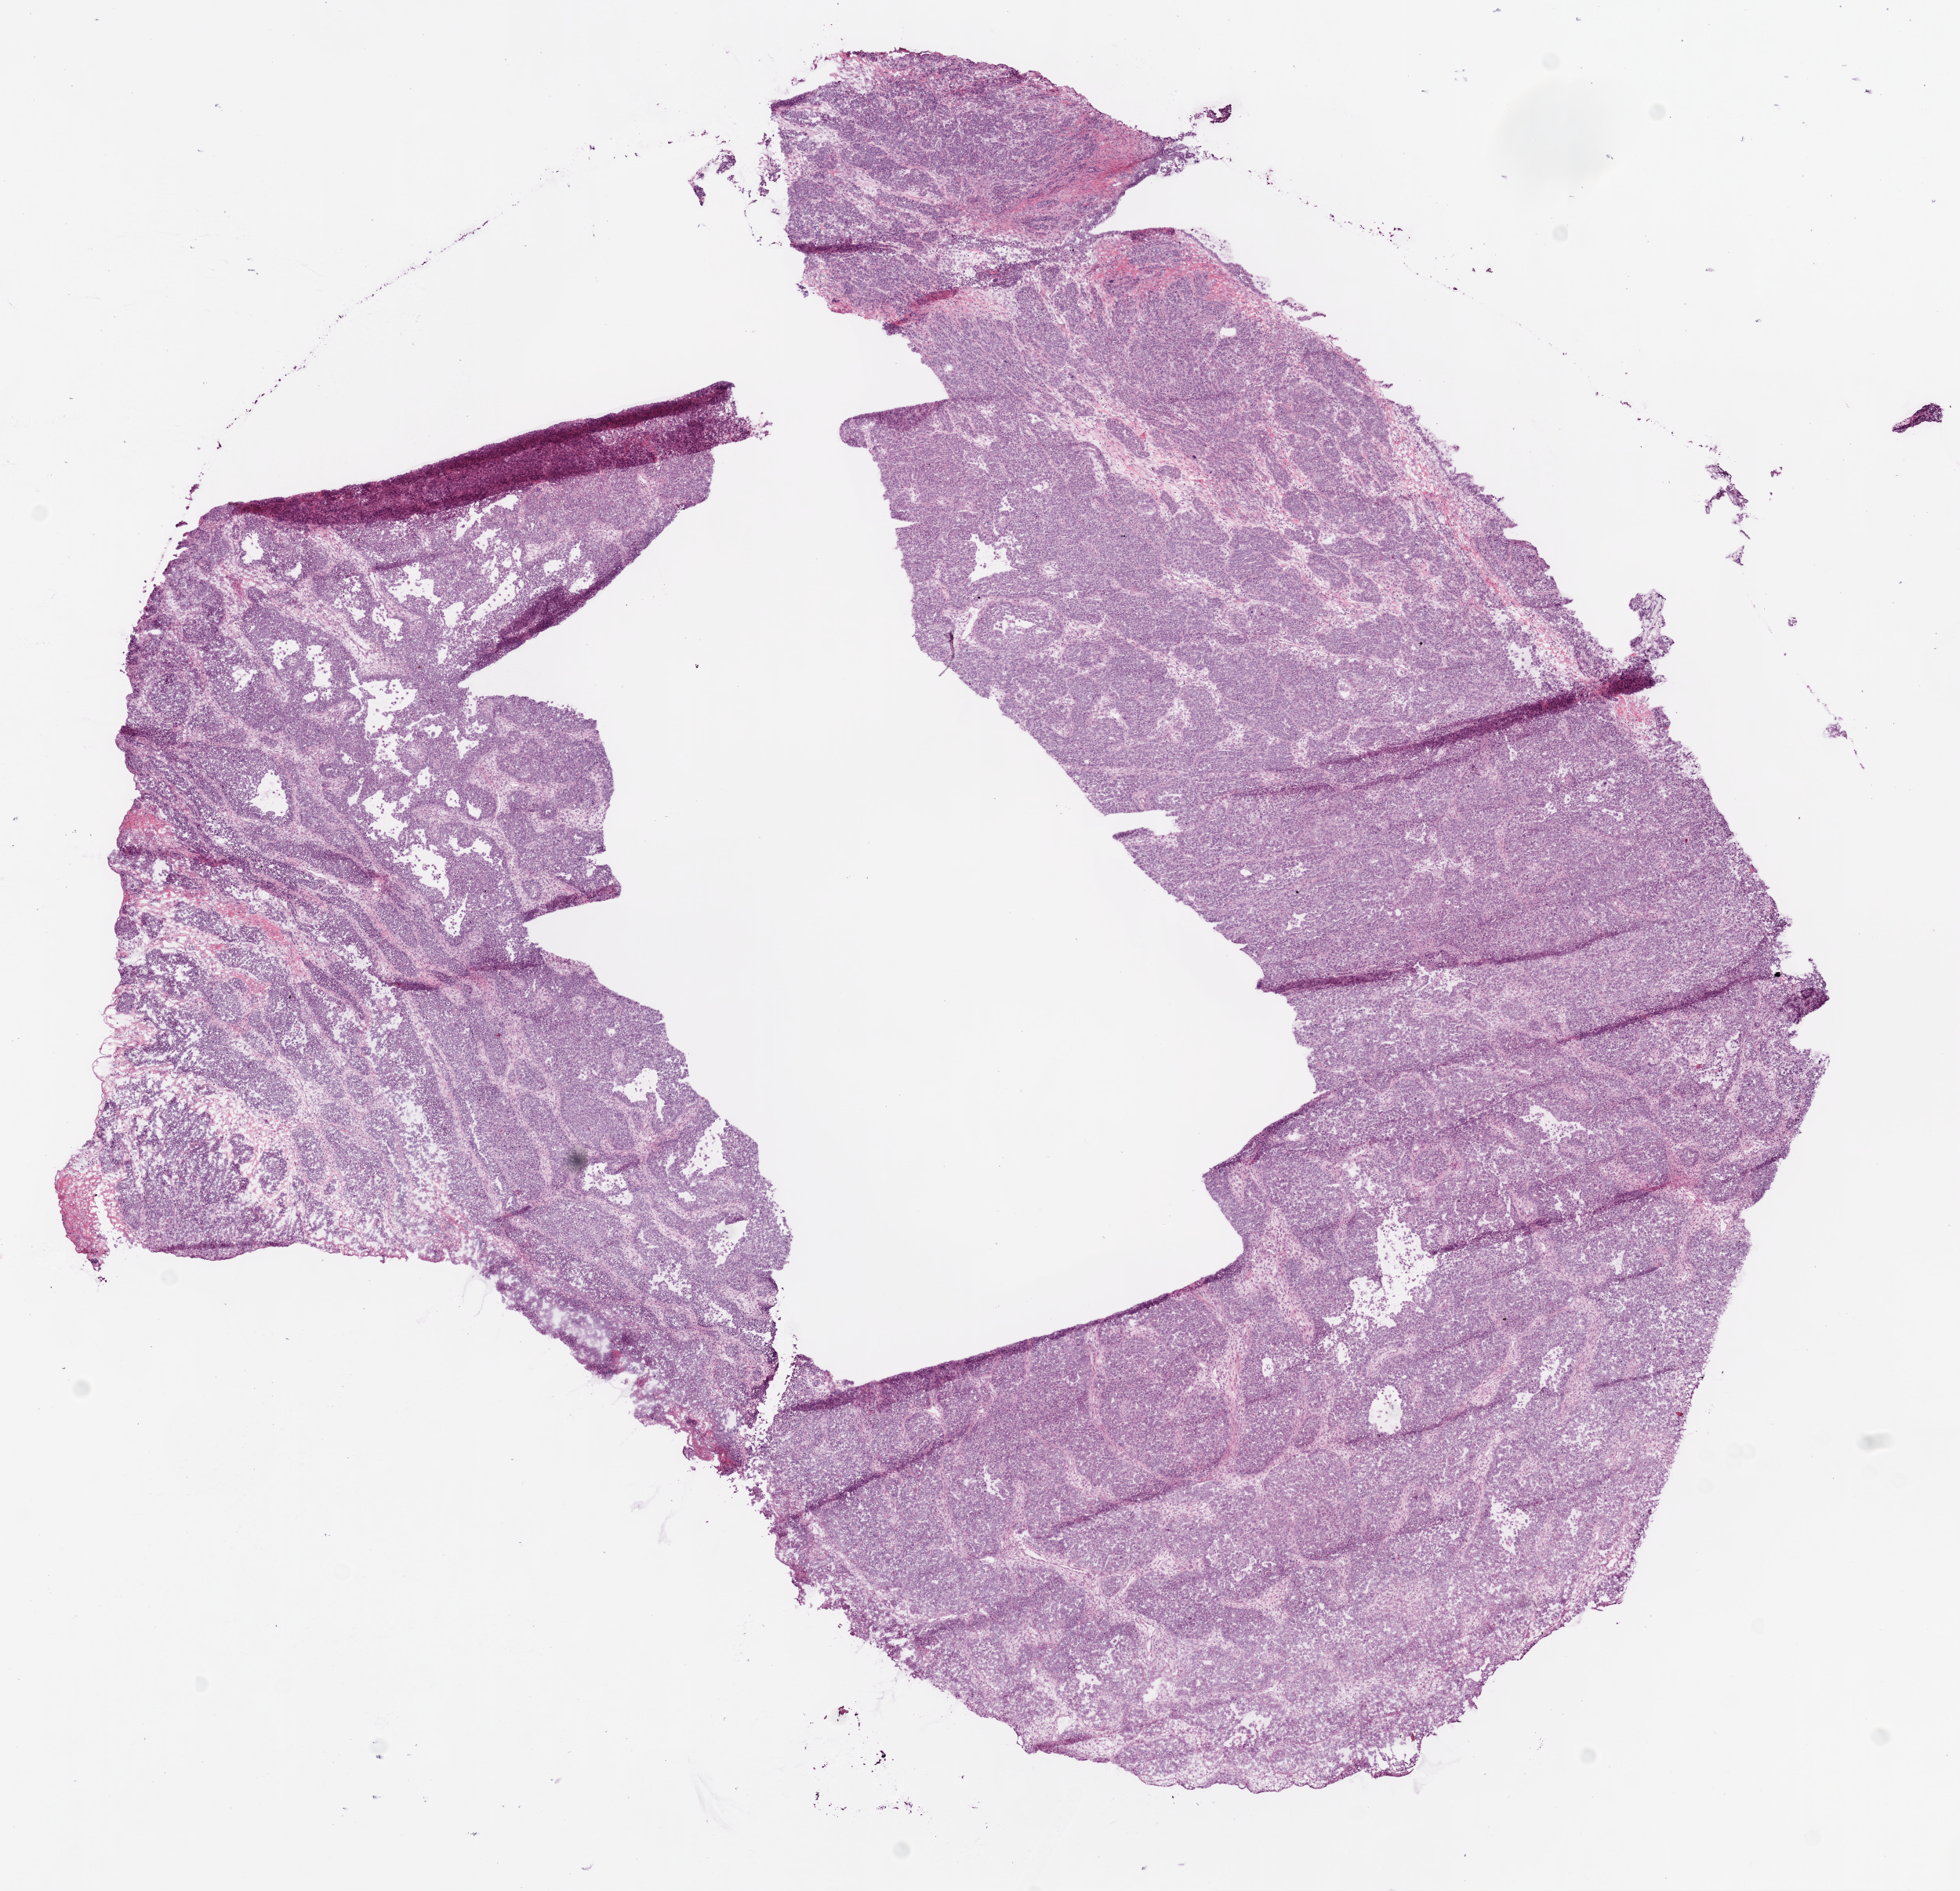
Whole-slide histology image, H&E — a low-resolution overview of the entire scanned area, about 10.0 x 9.7 mm (slide scanned at 20x); frozen section from the bottom of the tissue portion; ovary, primary tumour sample. Female patient; age at initial diagnosis 45 years. Histologic grade: G3 (poorly differentiated). Composition of this section per pathologist review: tumour cells 90%, tumour nuclei 95%, normal cells 0%, stromal cells 9%, necrosis 1%. Infiltration values recorded for this section: lymphocyte infiltration 1%.
FIGO stage: IIIC. Pathologic diagnosis: Serous cystadenocarcinoma, NOS.